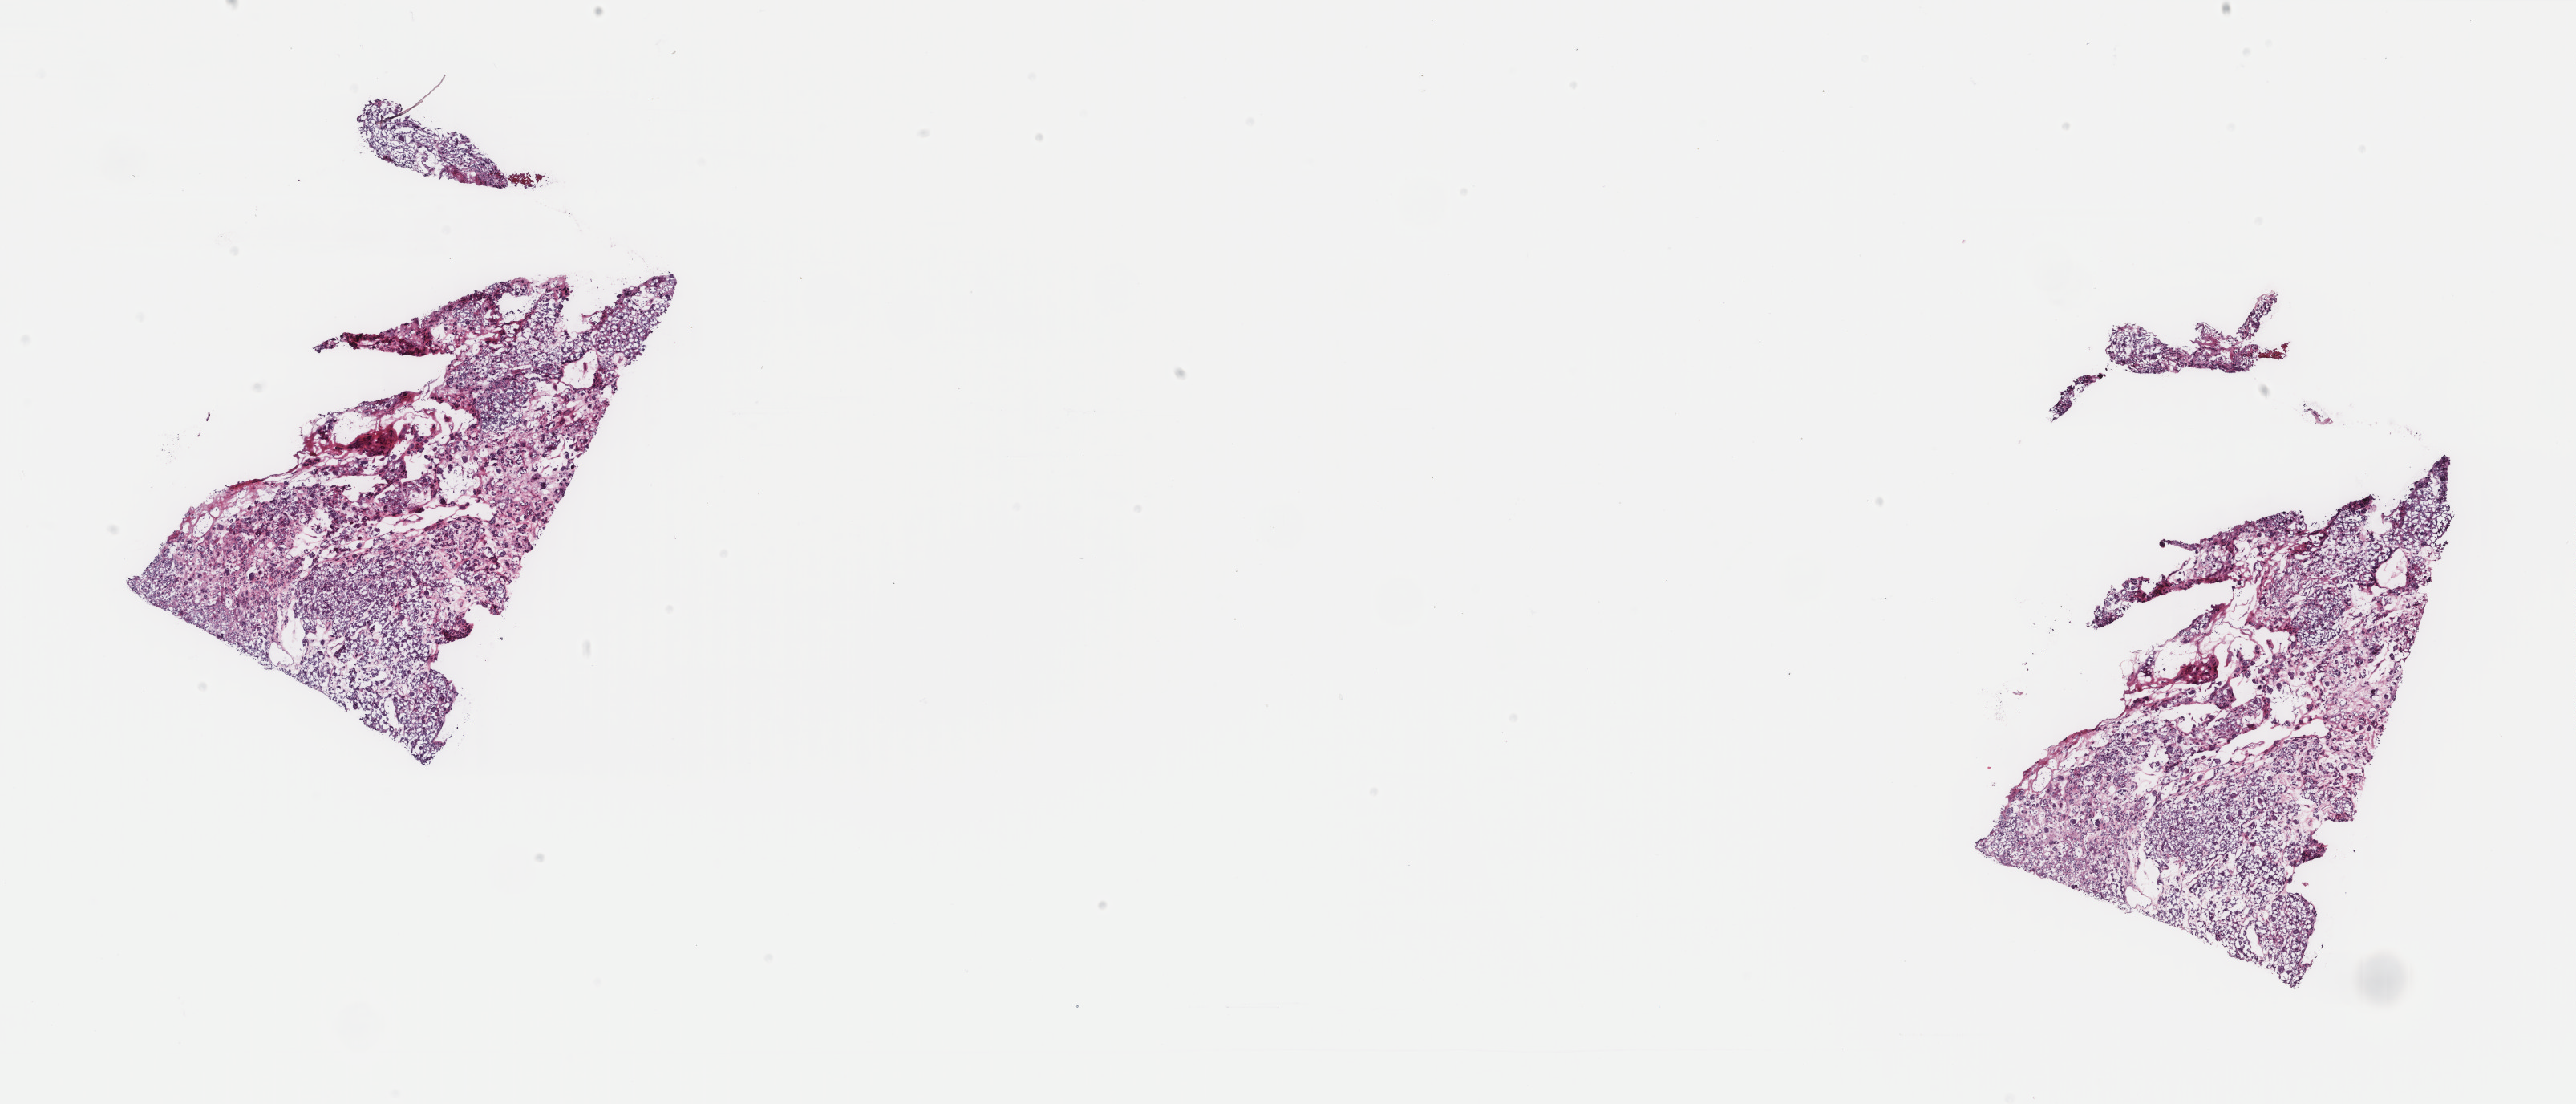
Hematoxylin and eosin (H&E) stained whole-slide image, whole scanned area (about 25.5 x 10.9 mm) shown as a low-resolution overview, frozen section from the top of the tissue portion, sample: primary tumour, thyroid. Patient: female, age at initial diagnosis 64 years. Pathologist review of this section (percent, as recorded): tumour cells 100%, tumour nuclei 92%, normal cells 0%, stromal cells 0%, necrosis 0%. Inflammatory infiltration, as recorded: lymphocyte infiltration 0%, monocyte infiltration 0%, neutrophil infiltration 0%.
- TNM: T1b N0 M0
- AJCC pathologic stage: I (7th edition)
- pathologic diagnosis: Papillary adenocarcinoma, NOS